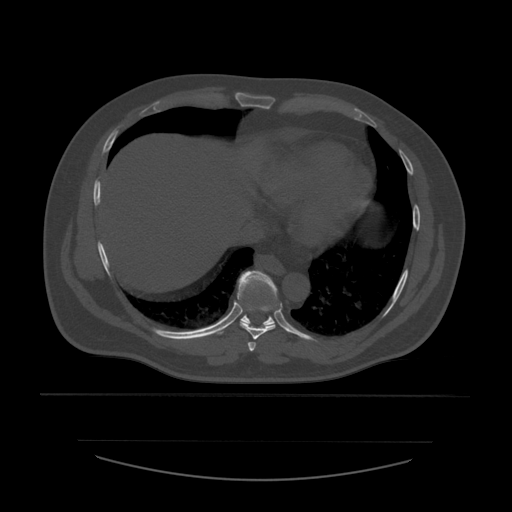
CT including the spine, one axial slice. Slice 330 of 532 in the series (ordered by position). Reconstruction kernel STANDARD. Bone window (W 1800 / L 400 HU). 512 × 512 image matrix. Patient age 44 years. Case-level facts recorded for this patient, not image findings: primary cancer: soft tissue sarcoma.
Outlined on this slice (semi-automatically segmented with operator editing):
- T7 vertebra: bounding box <248,342,257,353> (left, top, right, bottom; pixels)
- T8 vertebra: <240,321,276,340>
- T9 vertebra: <218,271,278,335>